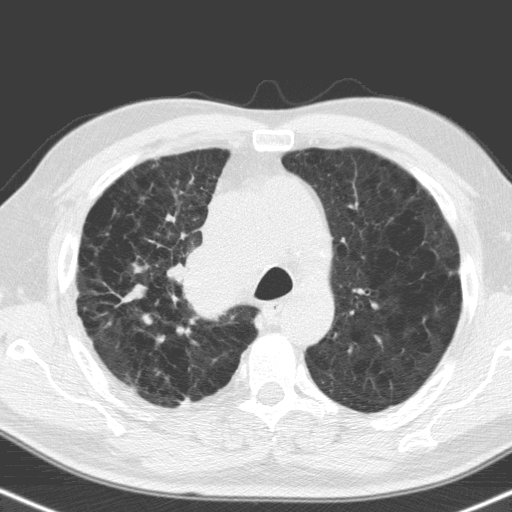
Low-dose screening chest CT, one axial slice. Position 121 of 160 along the scan axis. Lung window (W 1500 / L -600 HU). 3.2 mm slice thickness. 512 × 512 image matrix, field of view 324 × 324 mm.
Outlined on this slice (expert manual segmentation):
- lesion 1 (tumor, hilum of right lung): bounding box <170,246,244,318> (left, top, right, bottom; pixels)